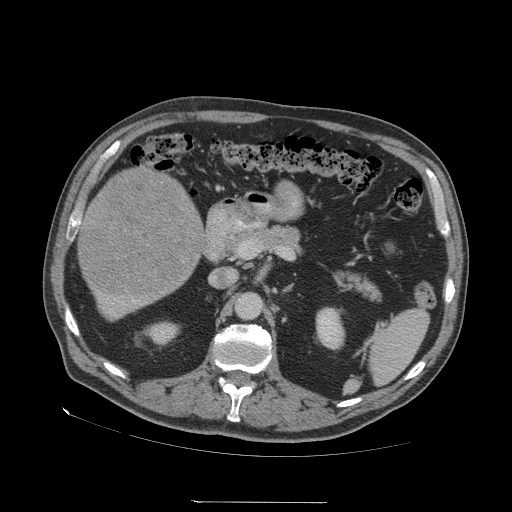
Contrast-enhanced abdominal CT (liver protocol), one axial slice; slice 18 of 83 in the series (ordered by position); reconstruction kernel STANDARD; soft-tissue window (W 400 / L 40 HU); 512 × 512 image matrix, field of view 460 × 460 mm. From the clinical record (not read from this slice): diagnosis: hepatocellular carcinoma (patient treated with transarterial chemoembolisation; whether this scan precedes or follows treatment is not stated here); TNM stage (as recorded): Stage-I; Child-Pugh class: A.
Outlined on this slice (semi-automatically segmented with operator editing):
- liver parenchyma outside the tumour (the mass and vessels are separate outlines, so this box may not span the whole liver): bounding box <78,166,206,317> (left, top, right, bottom; pixels)
- mass: <79,170,200,295>